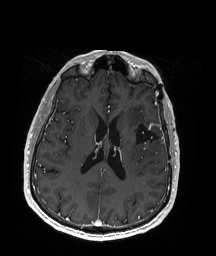
Brain MRI from a brain-tumour surgery series, one axial slice. Position 82 of 192 along the scan axis. T1-weighted post-contrast. 1 mm slice thickness. 216 × 256 image matrix, field of view 211 × 250 mm. Case-level facts recorded for this patient, not image findings: histopathology: Oligodendroglioma; WHO grade: 2; IDH mutation: yes.
Structures marked on this image (expert manual segmentation):
- previous resection cavity: bounding box <136,121,163,148> (left, top, right, bottom; pixels)